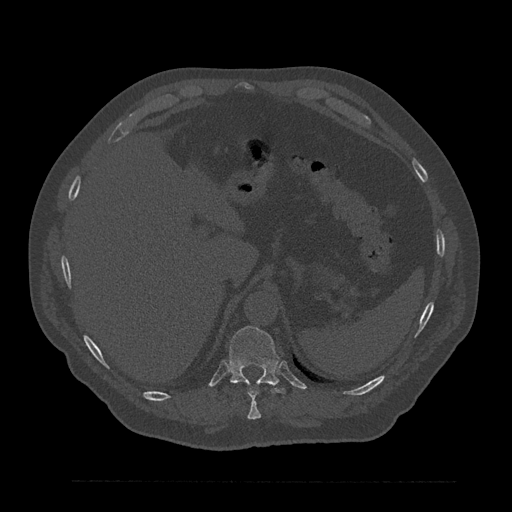
CT including the spine, one axial slice. Slice 315 of 797 in the series (ordered by position). 120 kVp. Bone window (W 1800 / L 400 HU). 512 × 512 image matrix. Male patient, age 61 years. Case-level facts recorded for this patient, not image findings: primary cancer: prostate.
Annotated regions visible in this slice (semi-automatic segmentation, software-assisted and operator-edited):
- T10 vertebra: bounding box <247,389,261,420> (left, top, right, bottom; pixels)
- T11 vertebra: <229,326,286,394>